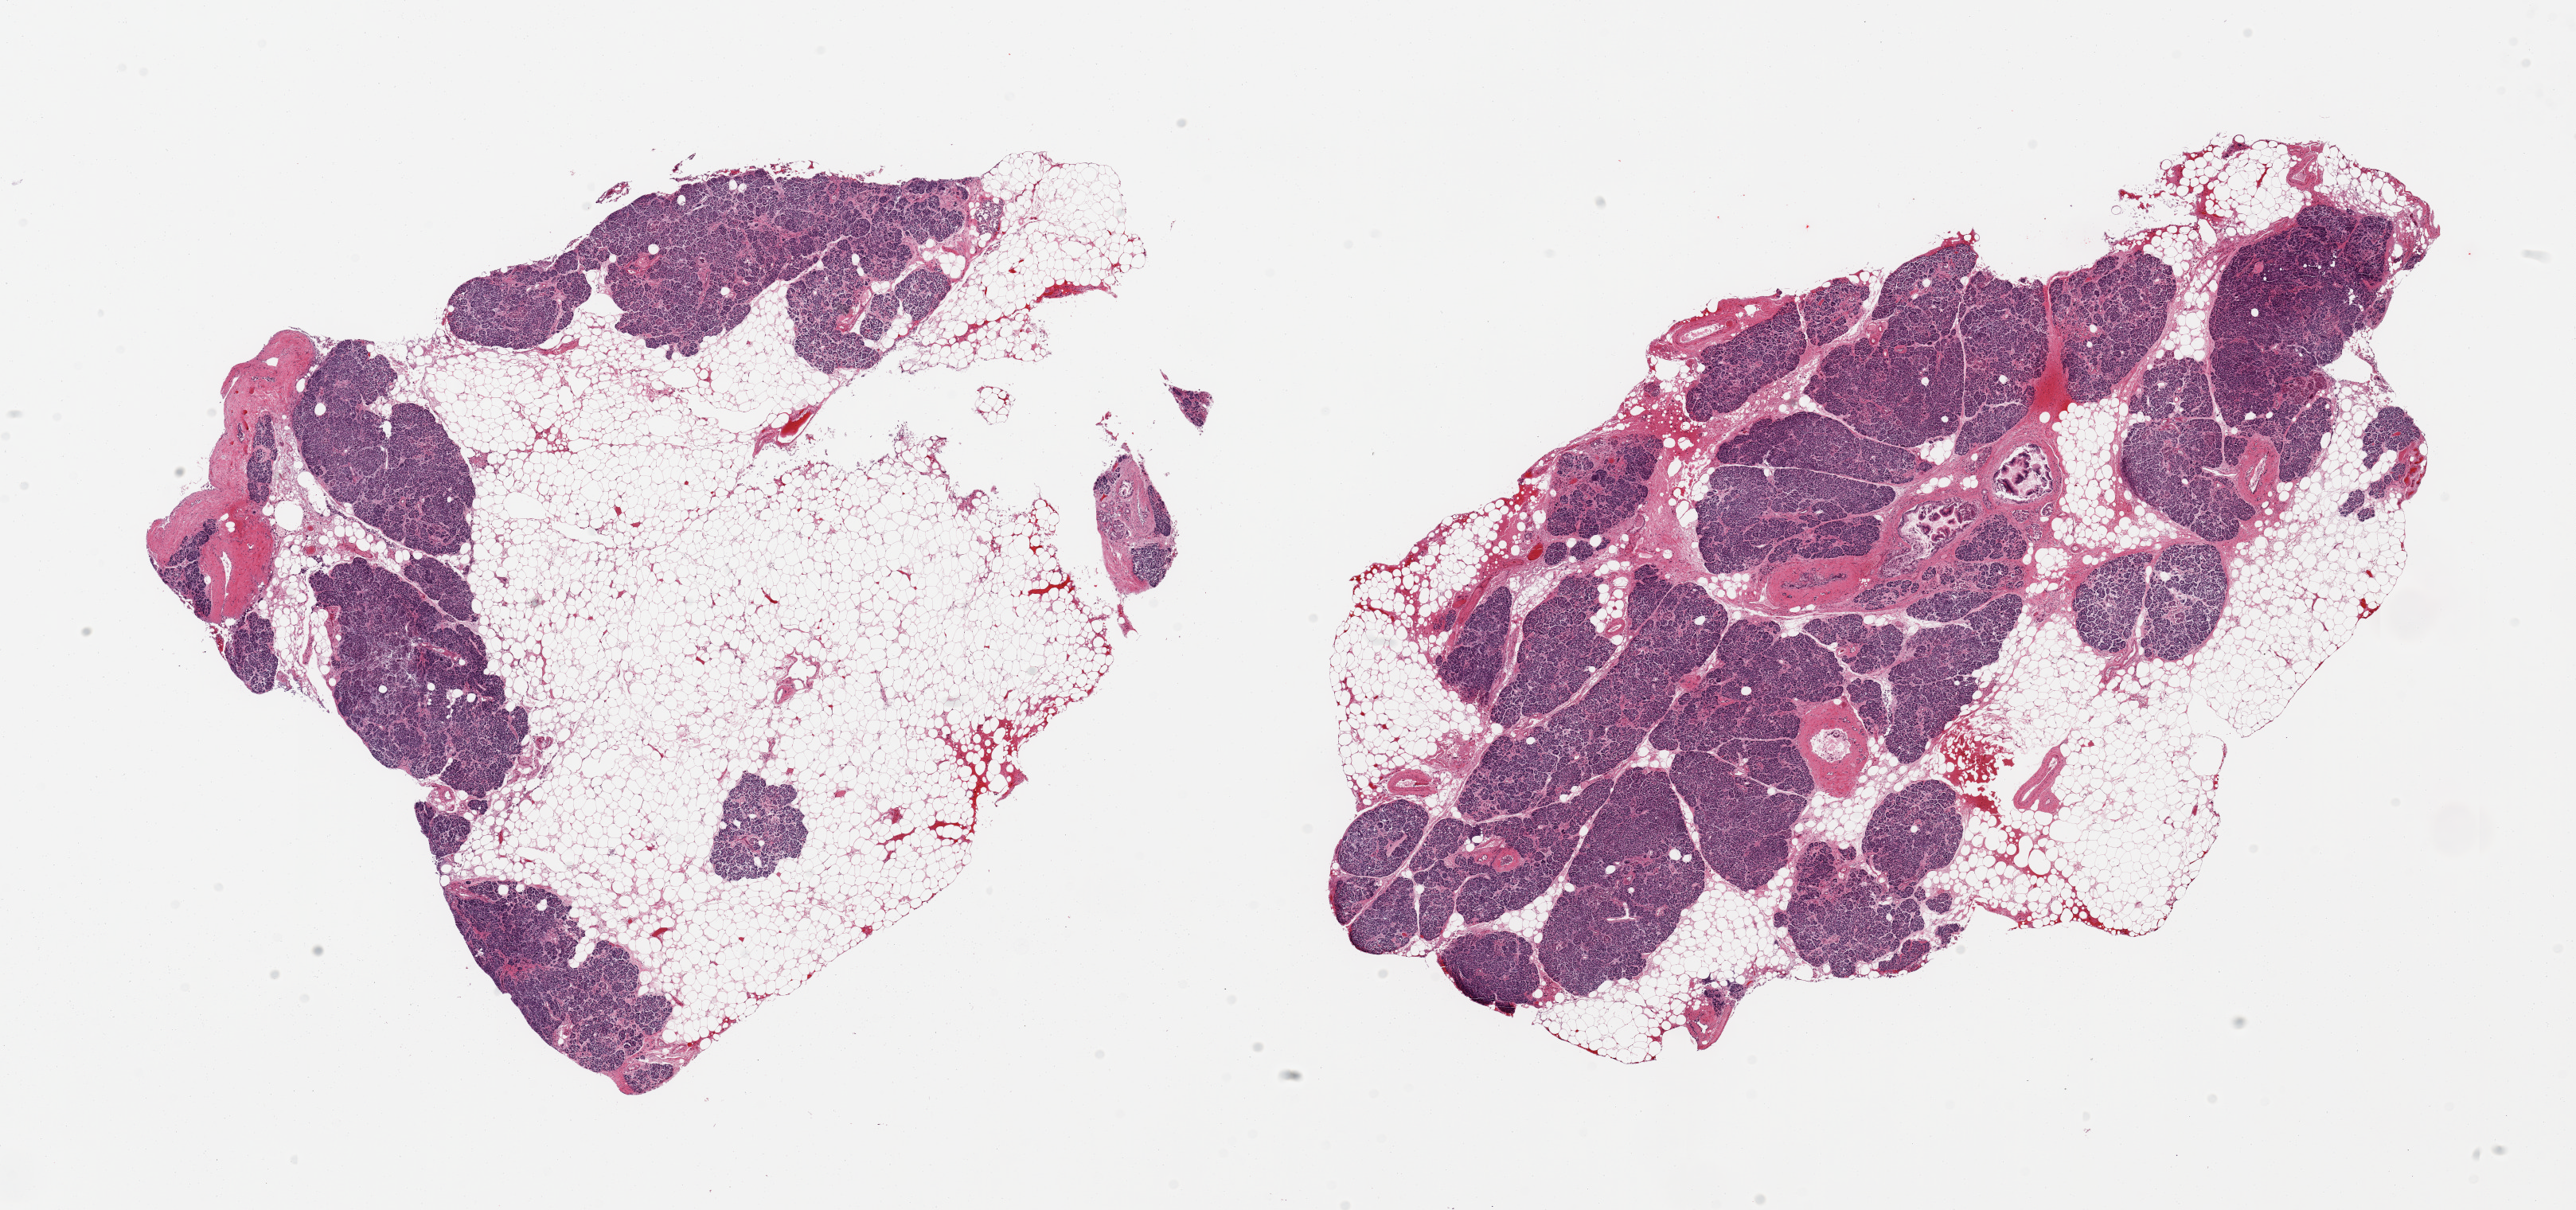
Digitized hematoxylin and eosin (H&E)-stained section — shown as a low-resolution overview of the whole scanned area (about 25.6 x 12.0 mm); PAXgene-fixed paraffin-embedded (PFPE) section; sampled site (target tissue): pancreas; tissue donor sample. Donor sex: female.
Pathologist's review note for this sample: 2 pieces; 80% and 40% internal/external fat, ? focal PanIN.